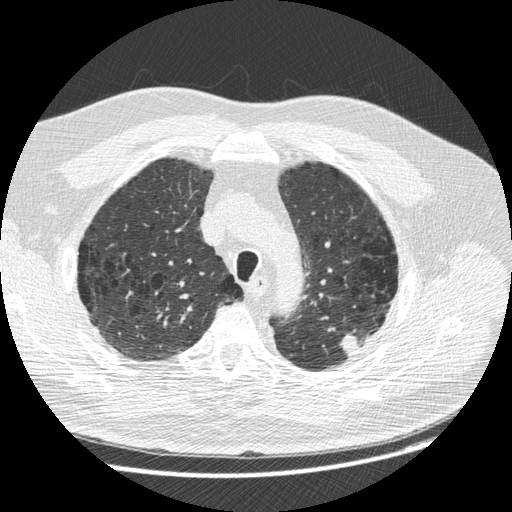
Low-dose screening chest CT, one axial slice. Position 205 of 258 along the scan axis. Reconstruction kernel STANDARD. 120 kVp. Lung window (W 1500 / L -600 HU). 1.25 mm slice thickness. 512 × 512 image matrix, field of view 370 × 370 mm.
Annotated regions visible in this slice (outlined manually by an expert reader):
- lesion 1 (tumor, upper lobe of left lung): bounding box (x1, y1, x2, y2) in pixels: (340, 333, 361, 355)